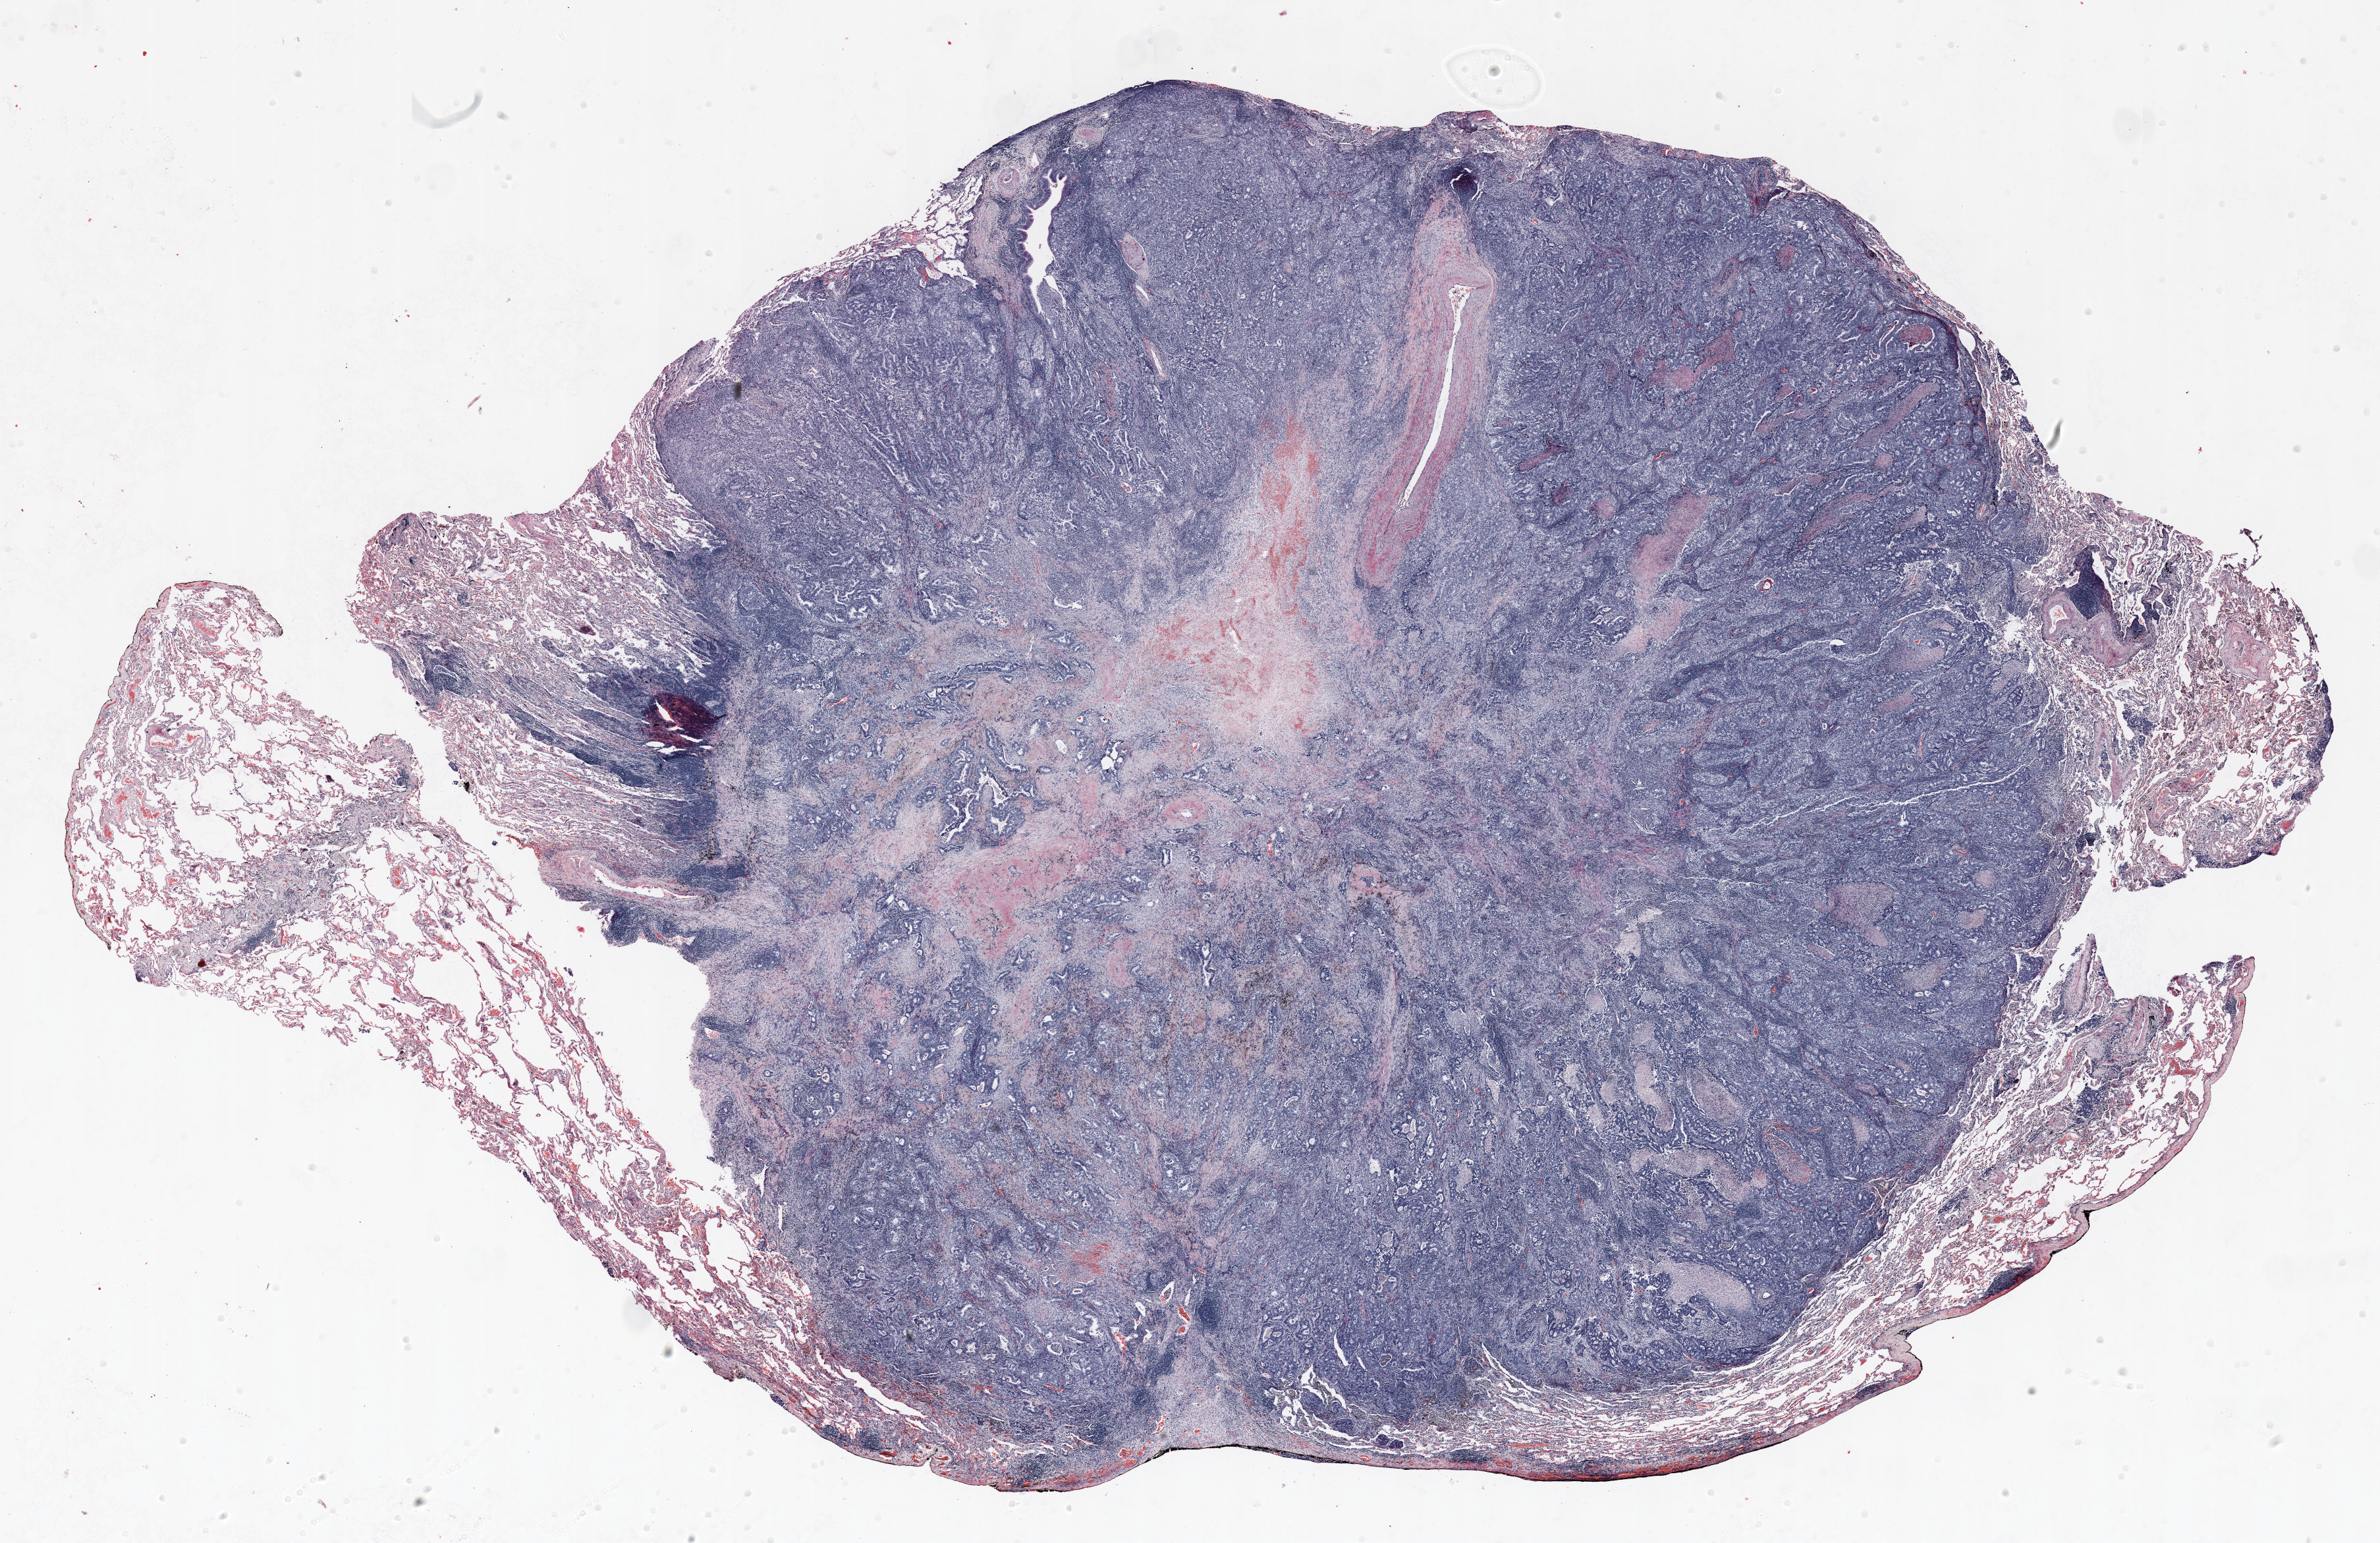
Whole-slide histology image, Hematoxylin and eosin (H&E) stained — low-resolution overview of the scanned area, about 29.0 x 18.8 mm. Formalin-fixed paraffin-embedded (FFPE) section. Lung tissue. Male, age 70 at enrolment. Current smoker at enrolment. Grade: poorly differentiated (G3).
* tumour size (pathology): 23 mm
* participant's lung-cancer diagnosis: Adenocarcinoma, NOS (ICD-O-3 8140/3)
* primary tumour location (clinical record): right upper lobe
* stage (AJCC 6th edition): IIA
* ICD-O-3 topography: upper lobe of lung (C34.1)